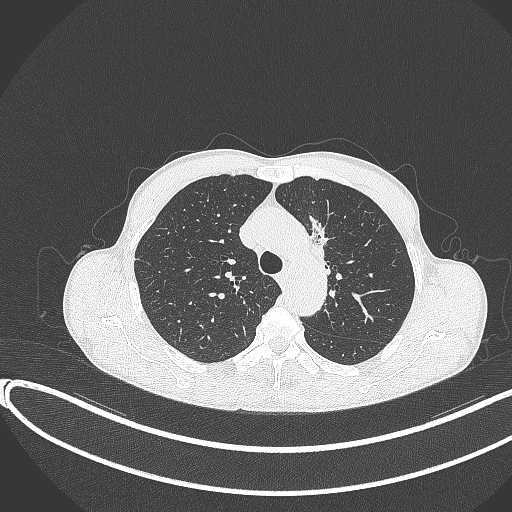
Chest CT, one axial slice; slice 275 of 374 in the series (ordered by position); reconstruction kernel B70f; 120 kVp; lung window (W 1500 / L -600 HU); 1 mm slice thickness; 512 × 512 image matrix, field of view 400 × 400 mm. Male patient, age 58 years. From the clinical record (not read from this slice): clinical TNM (as recorded): T1c N1 M0.
Structures marked on this image (bounding box drawn by a radiologist):
- lung tumour (recorded histology: adenocarcinoma): bounding box [x1, y1, x2, y2] px = [307, 211, 339, 268]